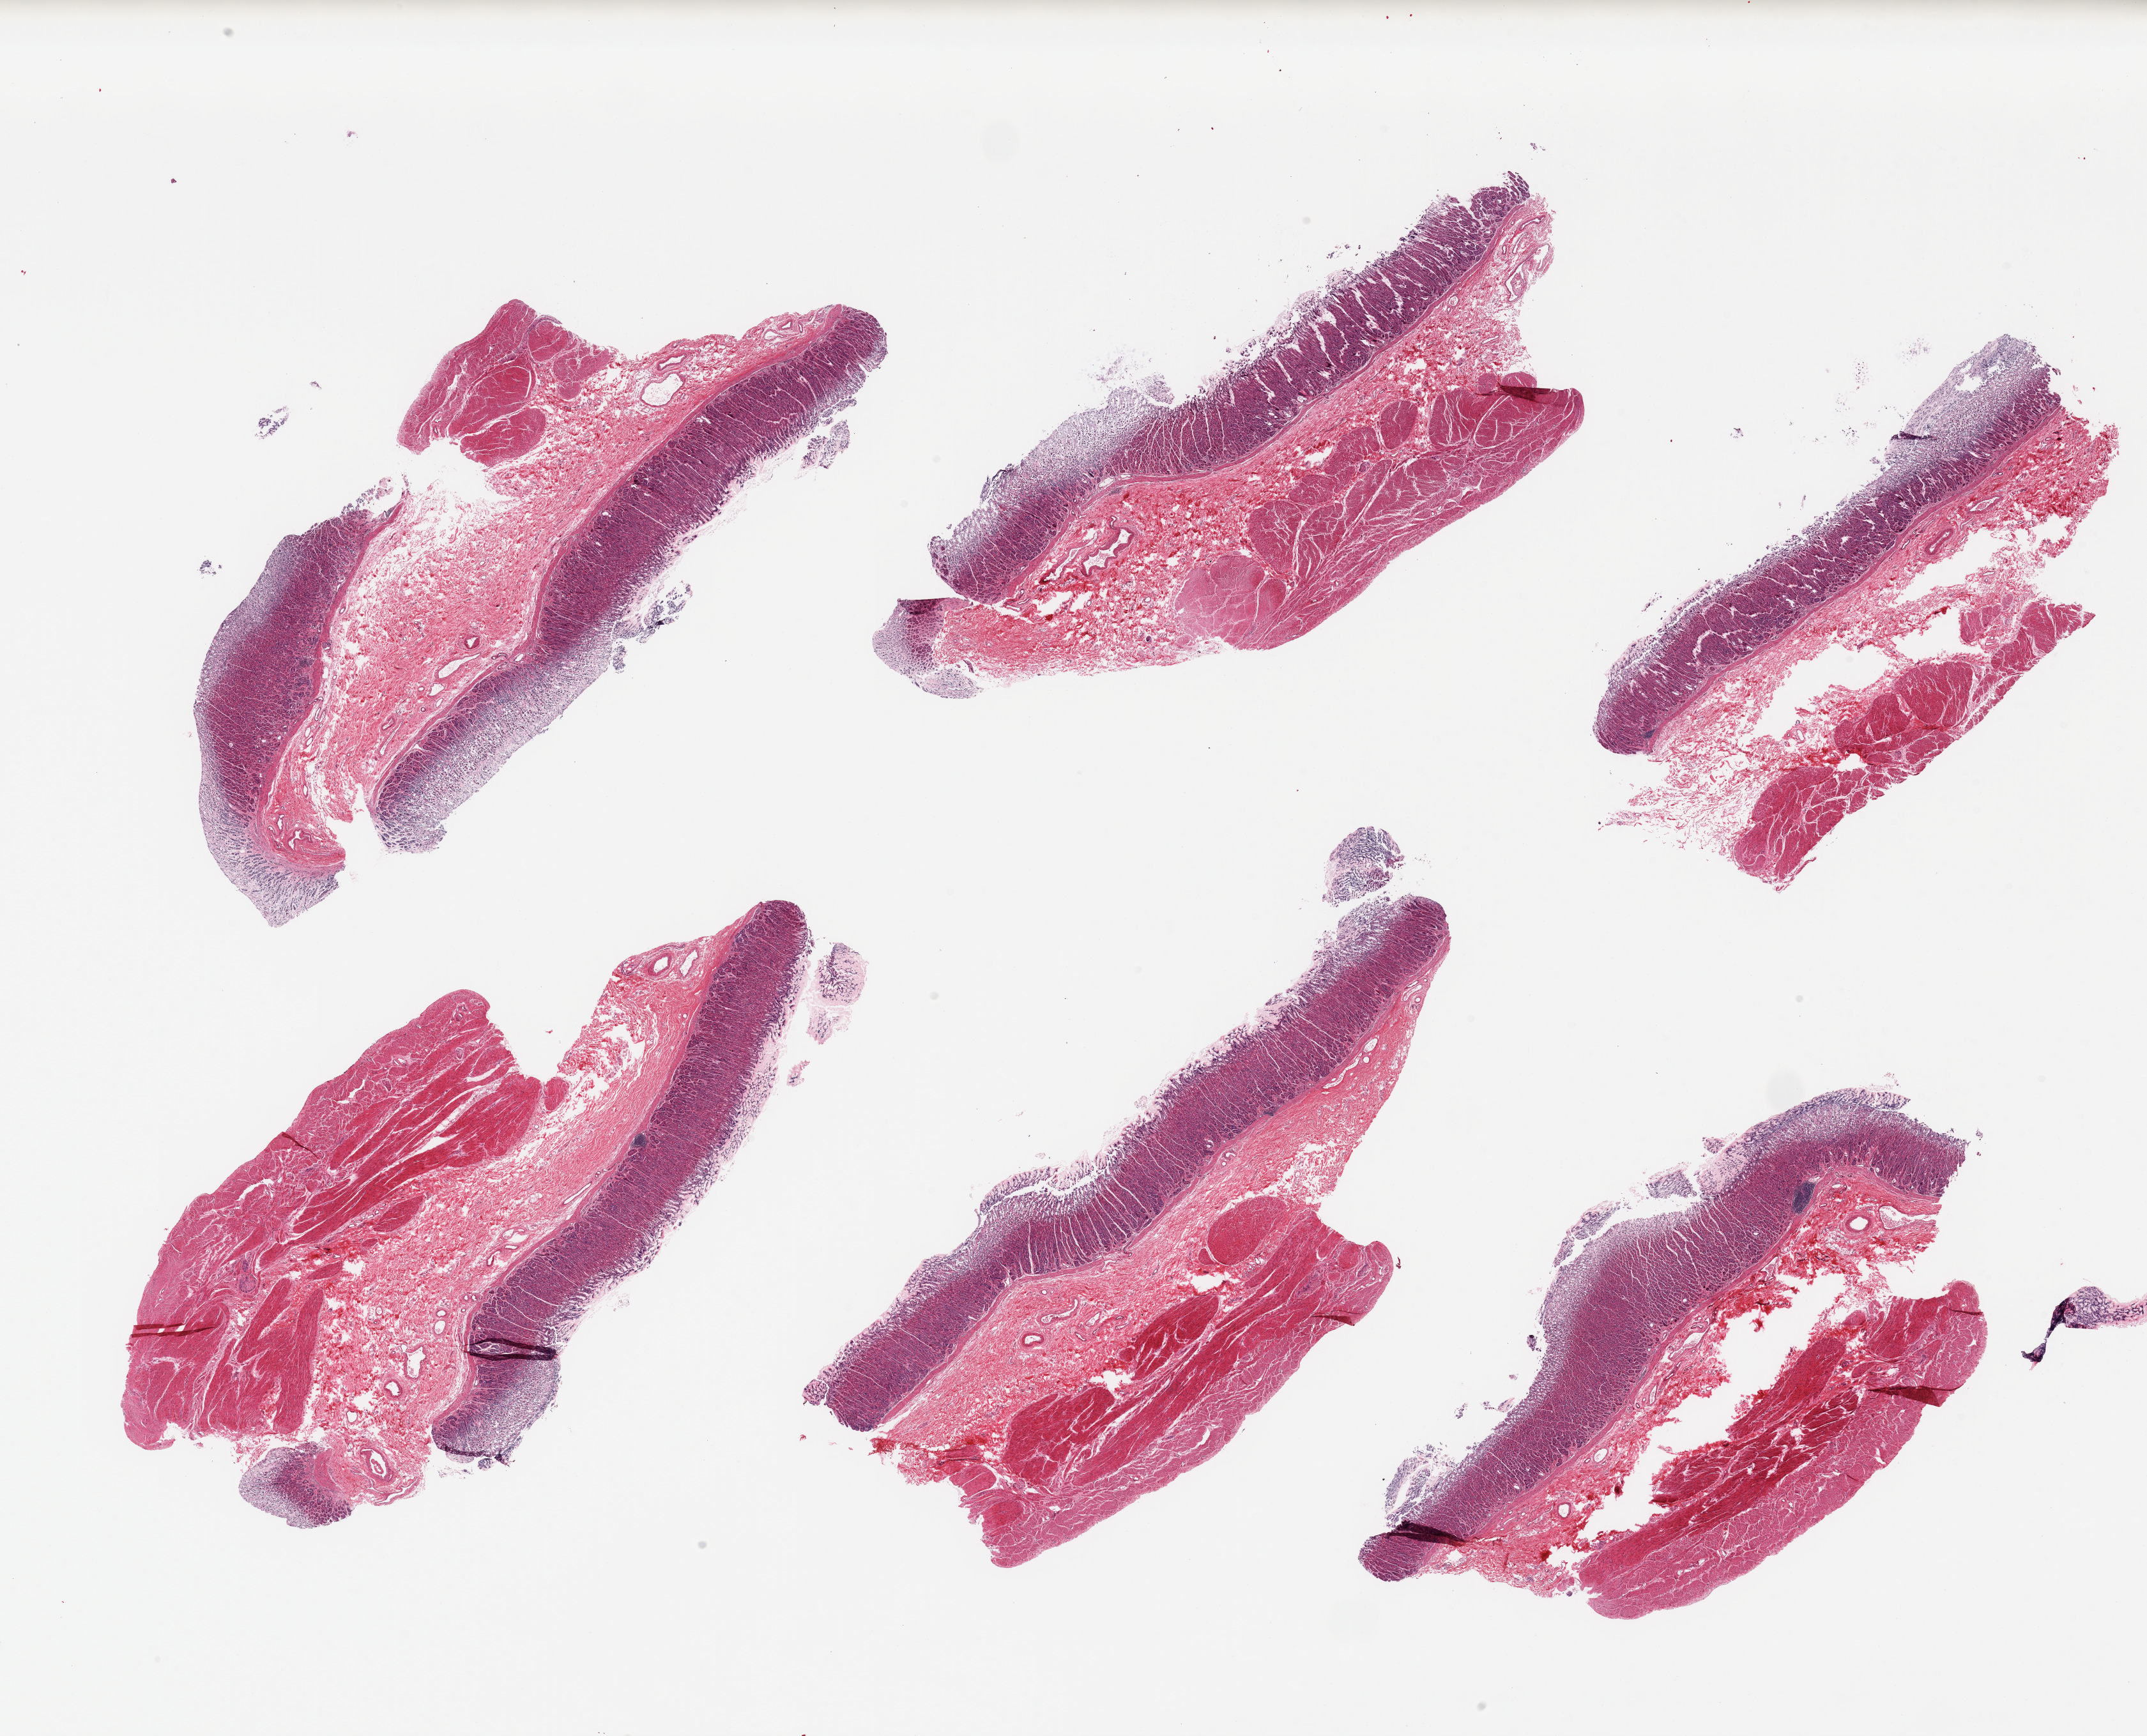
Whole-slide image, haematoxylin and eosin stain, brightfield — whole scanned area (about 26.6 x 21.5 mm) shown as a low-resolution overview; PAXgene-fixed paraffin-embedded (PFPE) section; target tissue: stomach; donor tissue sample. Donor sex: male.
Review note (as recorded): 6 pieces; mucosa and muscularis, few lymphoid aggregates.